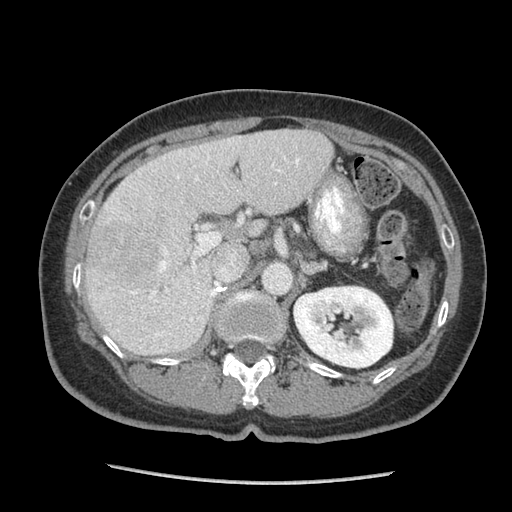
Contrast-enhanced abdominal CT (liver protocol), one axial slice. Position 48 of 105 along the scan axis. 140 kVp. Soft-tissue window (W 400 / L 40 HU). 512 × 512 image matrix, field of view 340 × 340 mm. Case-level facts recorded for this patient, not image findings: diagnosis: hepatocellular carcinoma (patient treated with transarterial chemoembolisation; whether this scan precedes or follows treatment is not stated here); TNM stage (as recorded): Stage-I; Child-Pugh class: A; tumour nodularity: uninodular; tumour size: 11.1 cm.
Outlined on this slice (semi-automatically segmented with operator editing):
- liver parenchyma outside the tumour (the mass and vessels are separate outlines, so this box may not span the whole liver): bounding box (x1, y1, x2, y2) in pixels: (86, 128, 332, 354)
- mass: (89, 212, 161, 281)
- liver vessels: (130, 140, 300, 337)